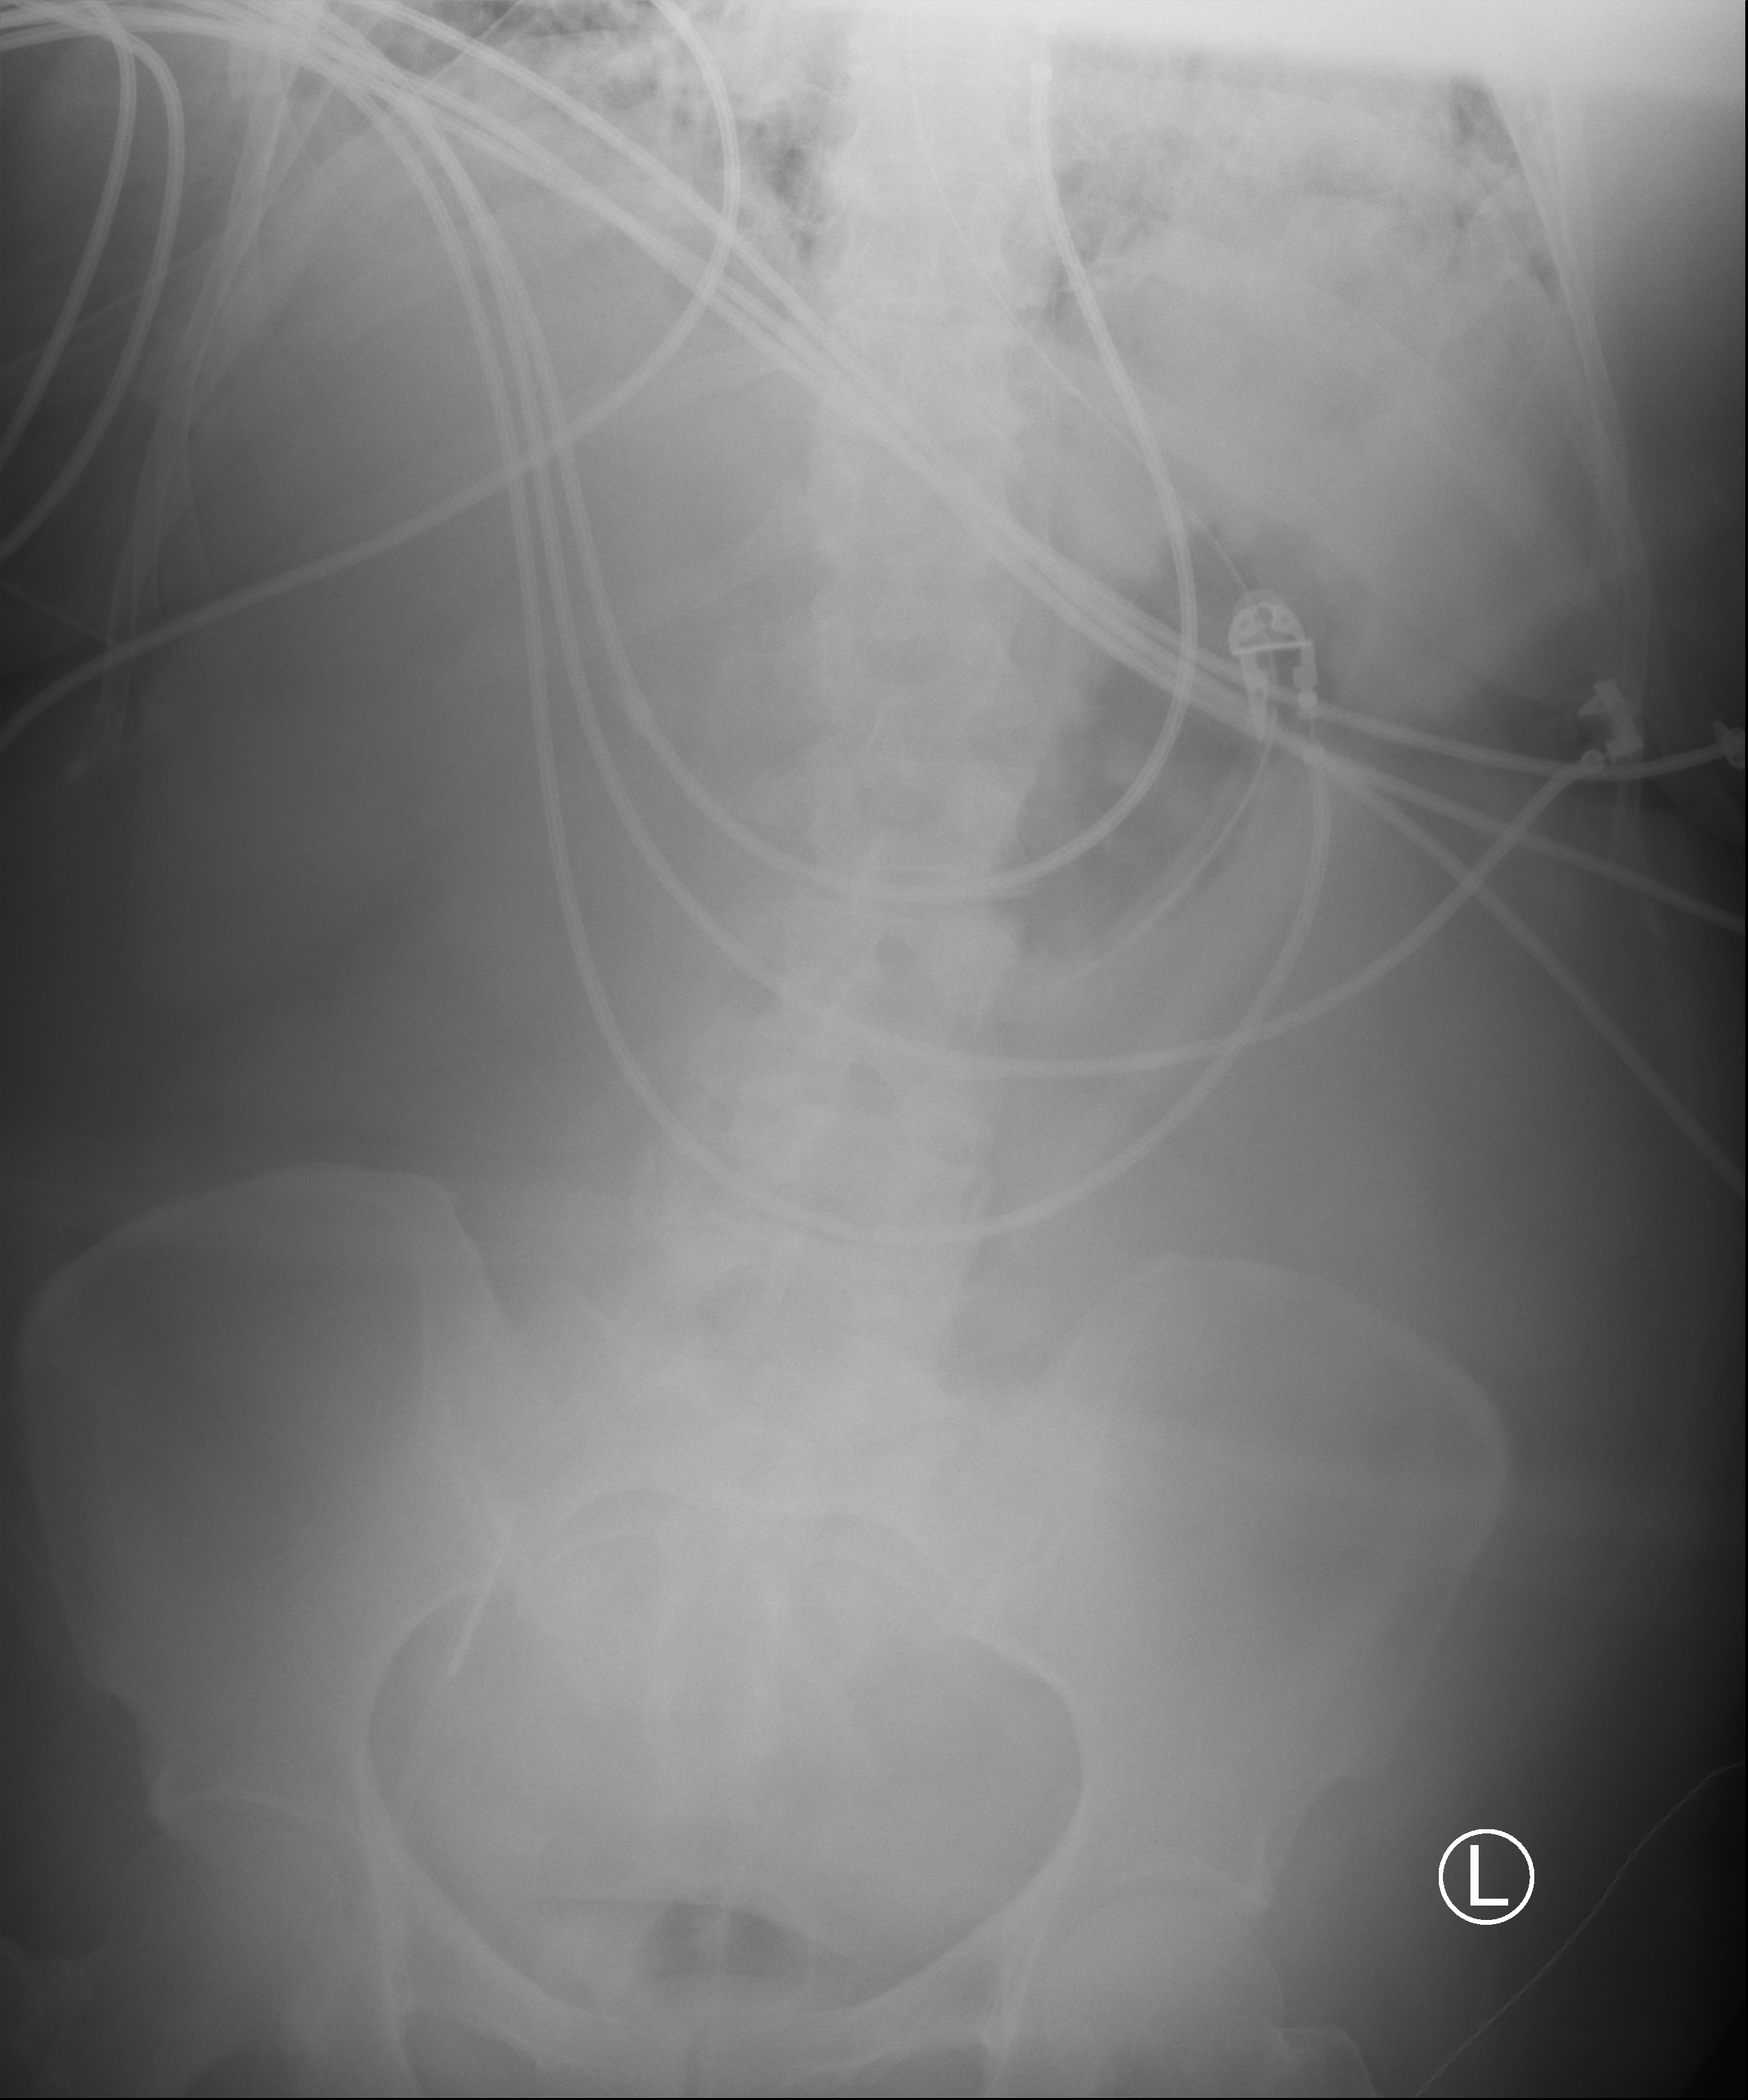
Portable abdomen radiograph, anteroposterior (AP) projection. Female patient hospitalised with COVID-19, age 60–74 years.
Admission-level facts for this patient (not findings on this image; timing relative to this image not recorded): admitted to intensive care during this hospital stay: yes; length of hospital stay: 45 days.